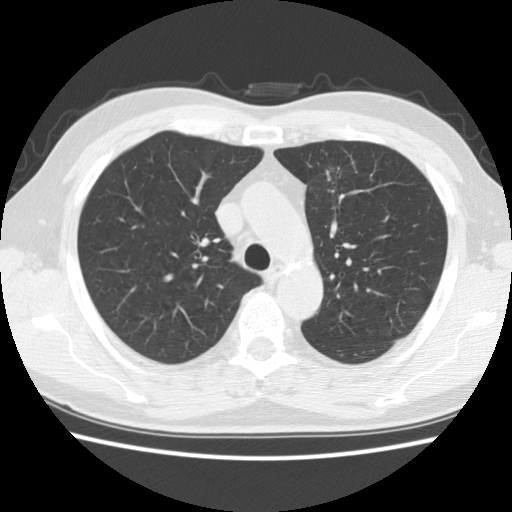
Low-dose screening chest CT, axial slice; second screening round (one year after baseline); lung window (W 1500 / L -600 HU); standard (soft-tissue) reconstruction kernel (STANDARD); 120 kVp; slice 50 of 172 in the series; 512 × 512 image matrix, field of view 337 × 337 mm. Male participant, aged 63 years at enrolment. Former smoker at enrolment.
Lesion marked by an expert reader, bounding box (x1, y1, x2, y2) in pixels: (300, 147, 356, 199). The exam's reader record, not a measurement of the box and not confirmed to be the same lesion: non-calcified nodule or mass ≥4 mm, left upper lobe, 23 × 18 mm, spiculated (stellate) margins, soft tissue attenuation, pre-existing on the prior screen: yes; interval growth: yes. Participant outcome: lung cancer diagnosed 83 days after this screen — adenocarcinoma, NOS, left upper lobe, moderately differentiated (G2), stage IA (AJCC 6th edition), 14 mm at pathology.